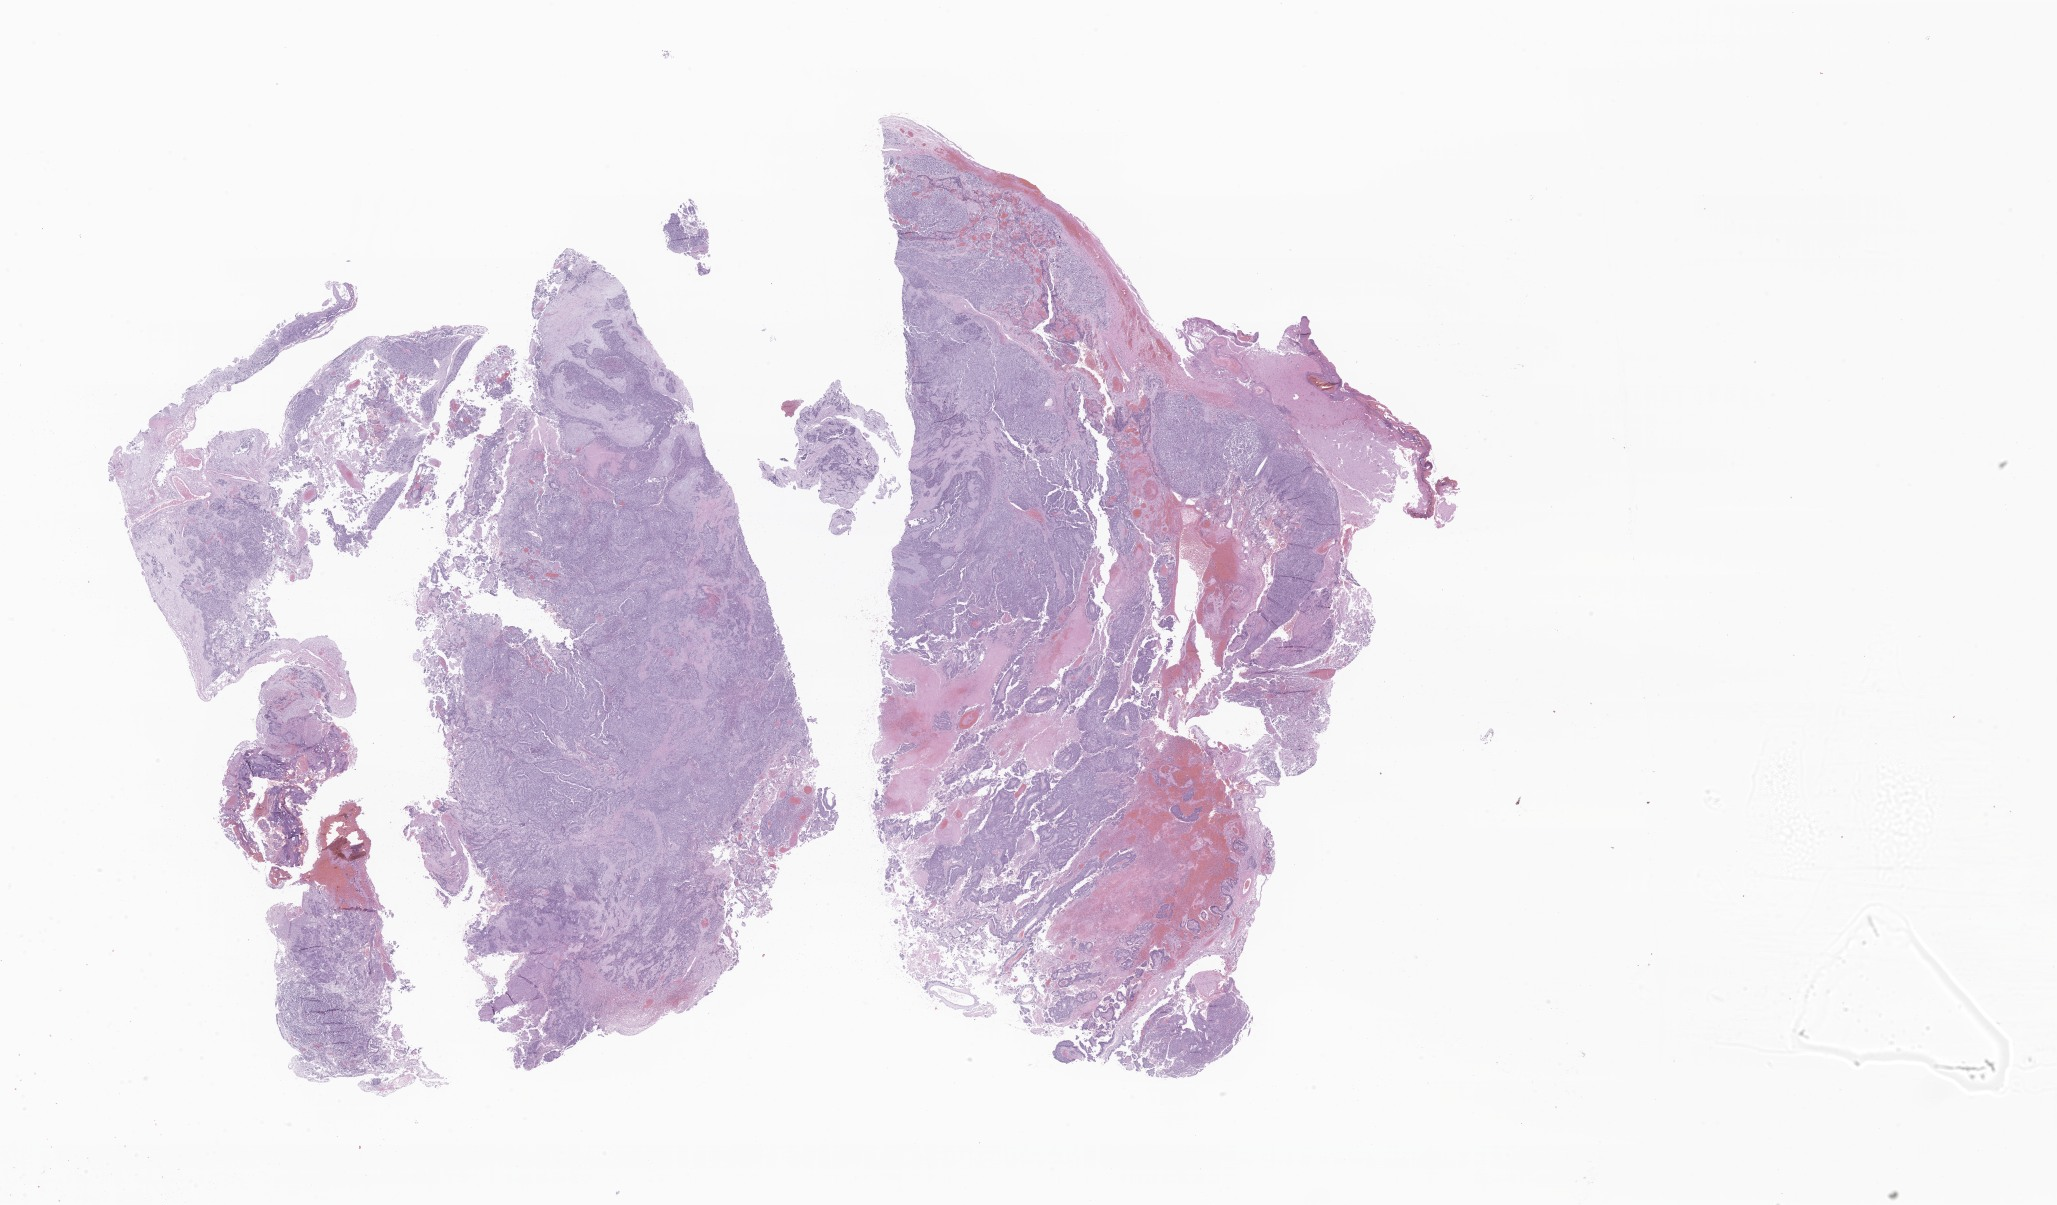
Whole-slide image, H&E stain of tumor tissue from the brain, low-resolution overview of the scanned area, about 34.7 x 20.3 mm. FFPE section. Patient female; age 149 months (12 years 5 months).
Diagnosis: Tumor cells, malignant.